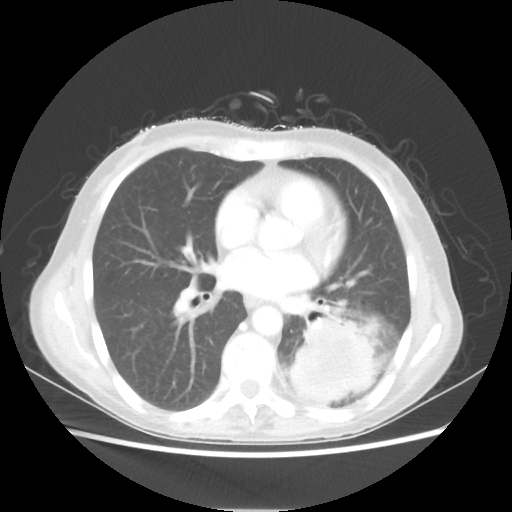
Chest CT, one axial slice; position 26 of 56 along the scan axis; 80 kVp; lung window (W 1500 / L -600 HU); 5 mm slice thickness; 512 × 512 image matrix, field of view 360 × 360 mm. Female patient, age 53 years. Case-level facts recorded for this patient, not image findings: clinical TNM (as recorded): T3 N0 M0.
Annotated regions visible in this slice (bounding box drawn by a radiologist):
- lung tumour (recorded histology: adenocarcinoma): box from (x=292, y=316) to (x=380, y=401) px